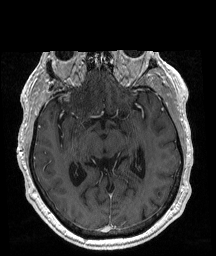
Brain MRI from a brain-tumour surgery series, one axial slice. Position 110 of 192 along the scan axis. T1-weighted post-contrast. 1 mm slice thickness. 216 × 256 image matrix. From the clinical record (not read from this slice): histopathology: Glioblastoma; WHO grade: 4; IDH mutation: no; tumour location: Right Frontal.
Structures marked on this image (manually delineated by an expert):
- tumour: bounding box (x1, y1, x2, y2) in pixels: (41, 89, 60, 100)